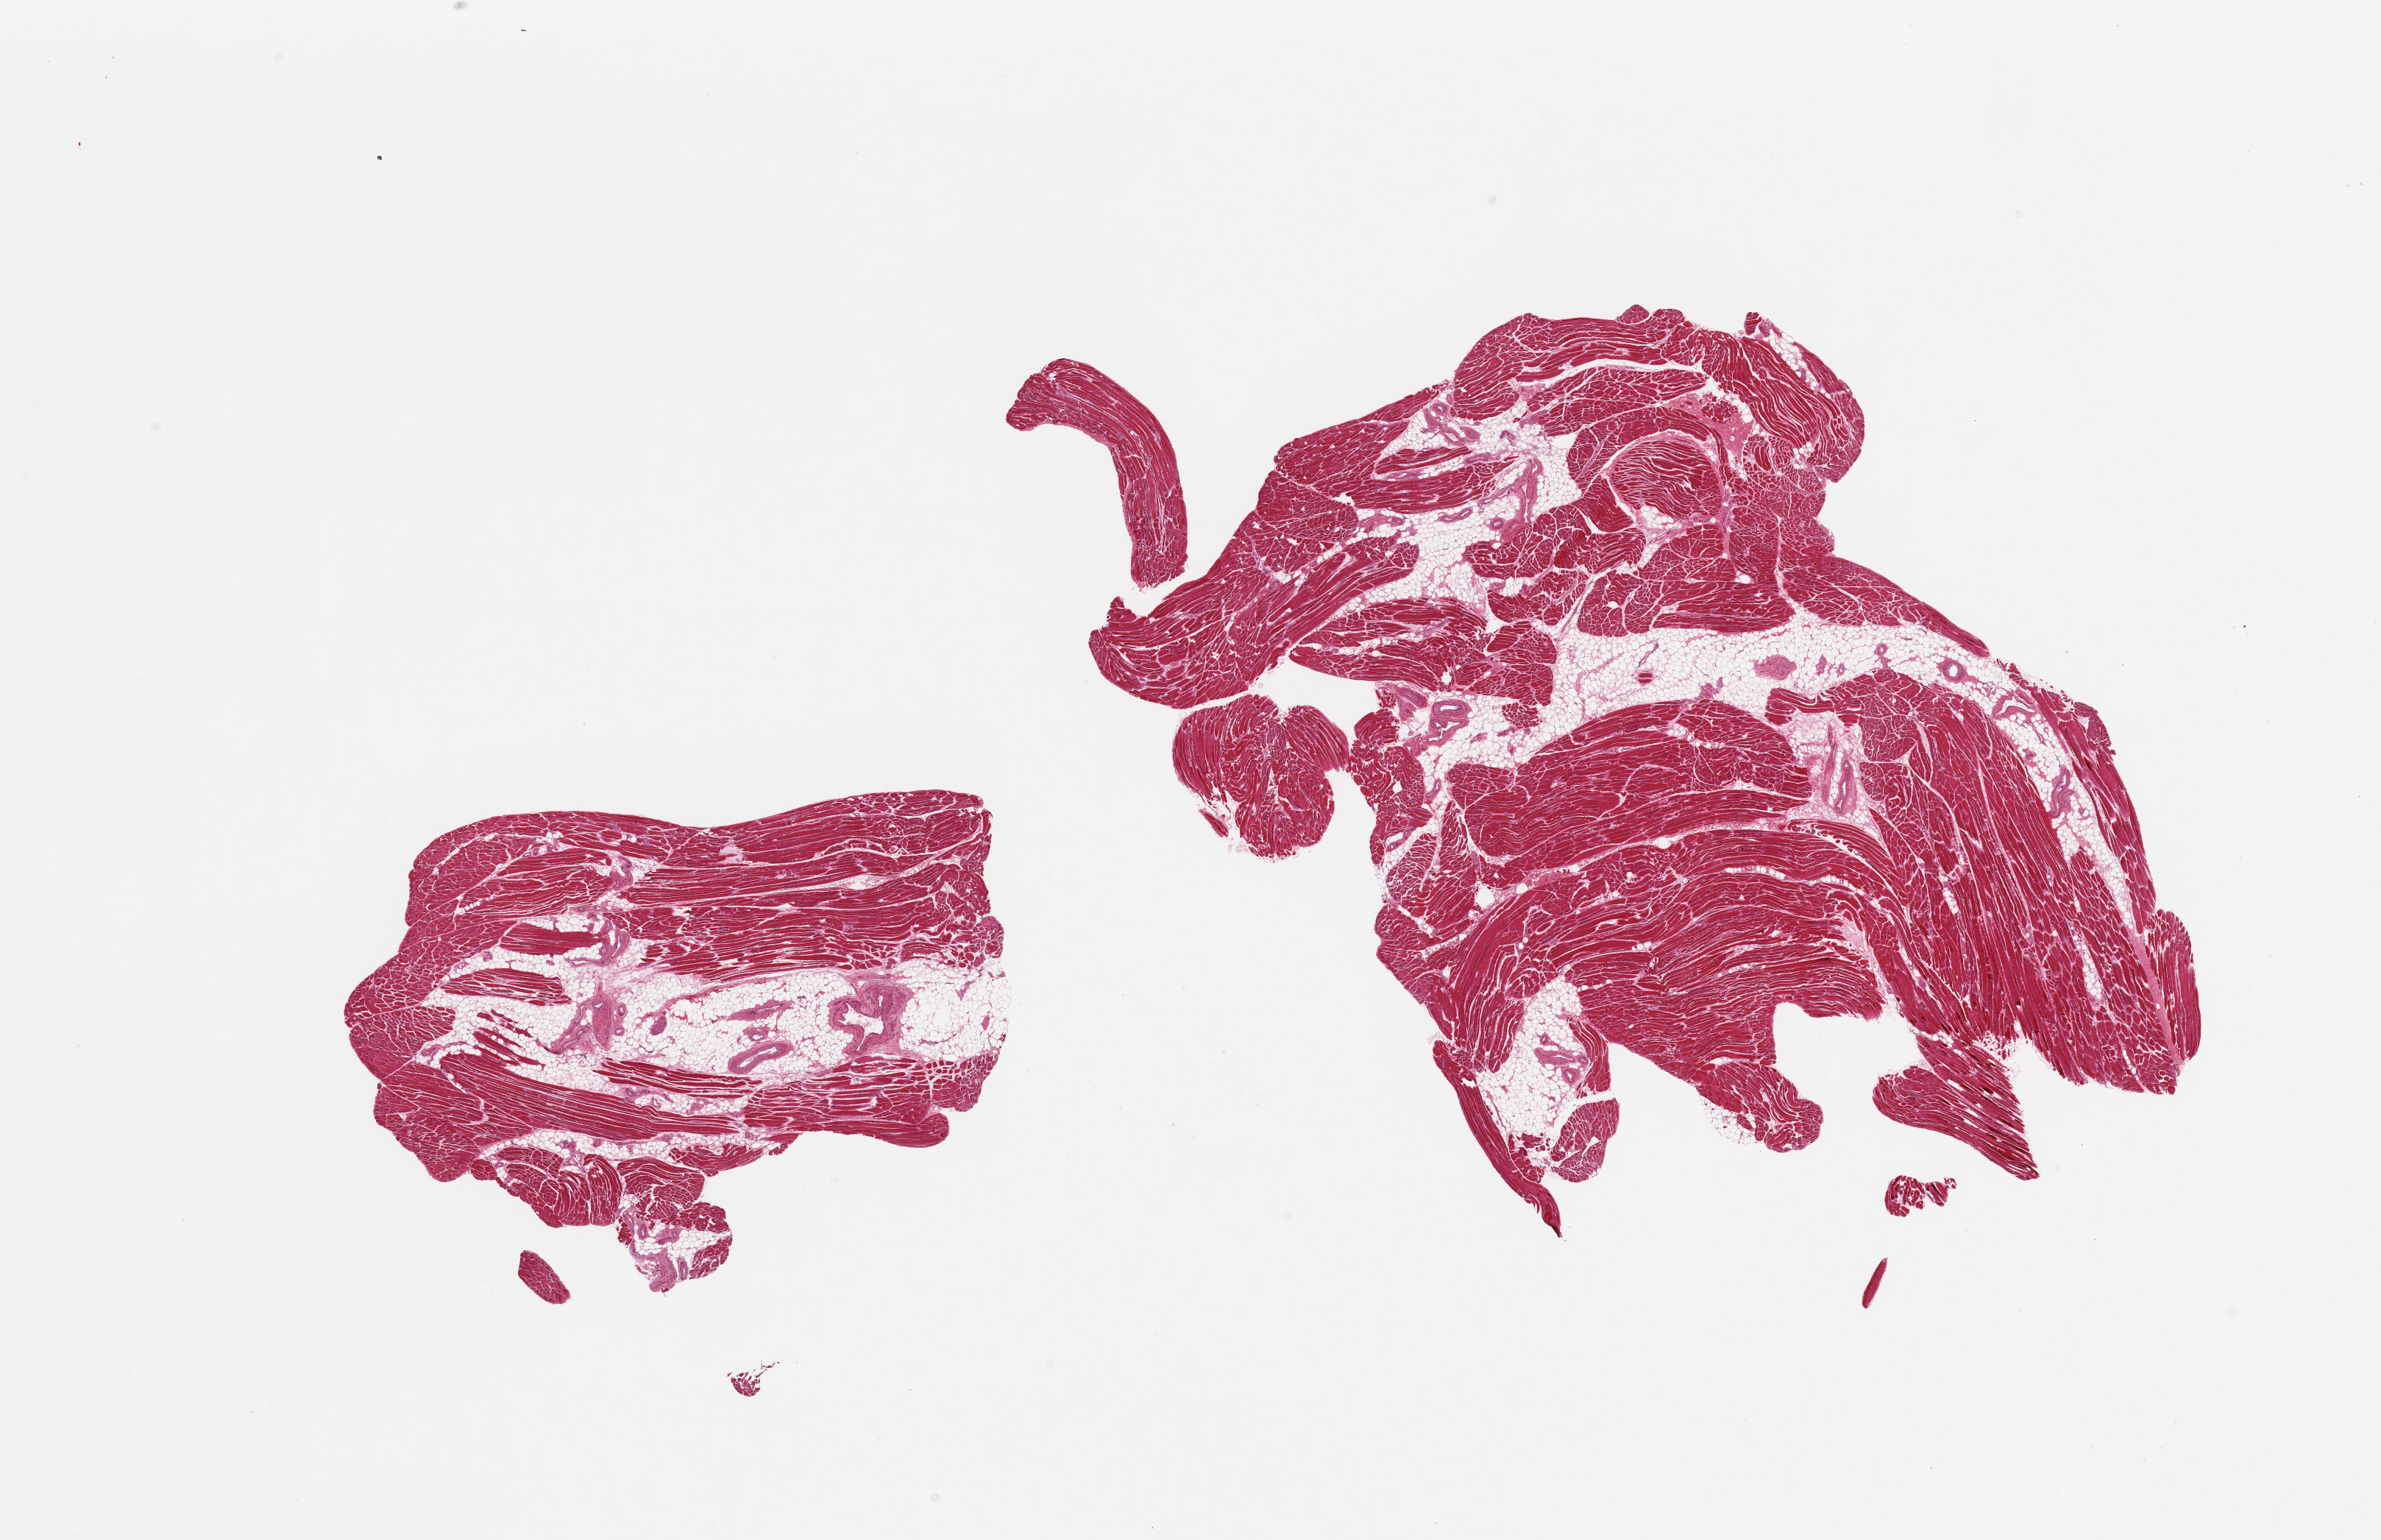
Hematoxylin and eosin (H&E) whole-slide image, shown as a low-resolution overview of the whole scanned area (about 25.6 x 16.6 mm, from a 20x scan). PAXgene-fixed paraffin-embedded (PFPE) section. Section of skeletal muscle (target tissue). Donor tissue sample. Donor sex: male.
Review note (as recorded): 2 pieces; up to 30% internal fat, some atrophic fibers.